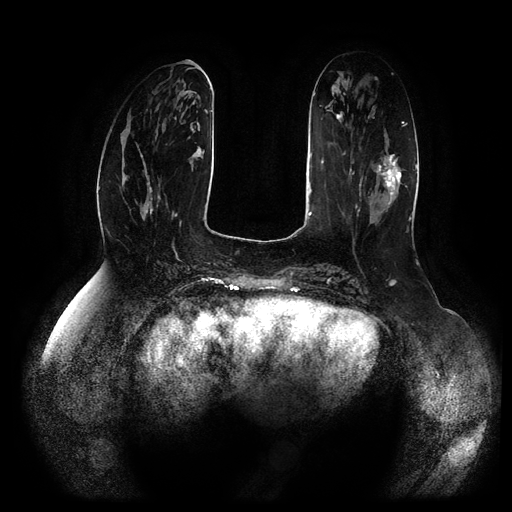
Breast MRI (dynamic contrast-enhanced, multi-phase), one axial slice; position 34 of 116 along the scan axis; dynamic contrast-enhanced series, time point 2 of 5 at this slice position (early post-contrast); 1.5 T; TE 2.5 ms, TR 5.2 ms; 2 mm slice thickness; 512 × 512 image matrix, field of view 400 × 400 mm. Patient: female, 66 years.
Structures marked on this image (semi-automatically segmented with operator editing):
- breast lesion (labelled 'tumour' in the annotation; benign lesions carry a separate 'benign' label): bounding box [x1, y1, x2, y2] px = [375, 154, 402, 205]